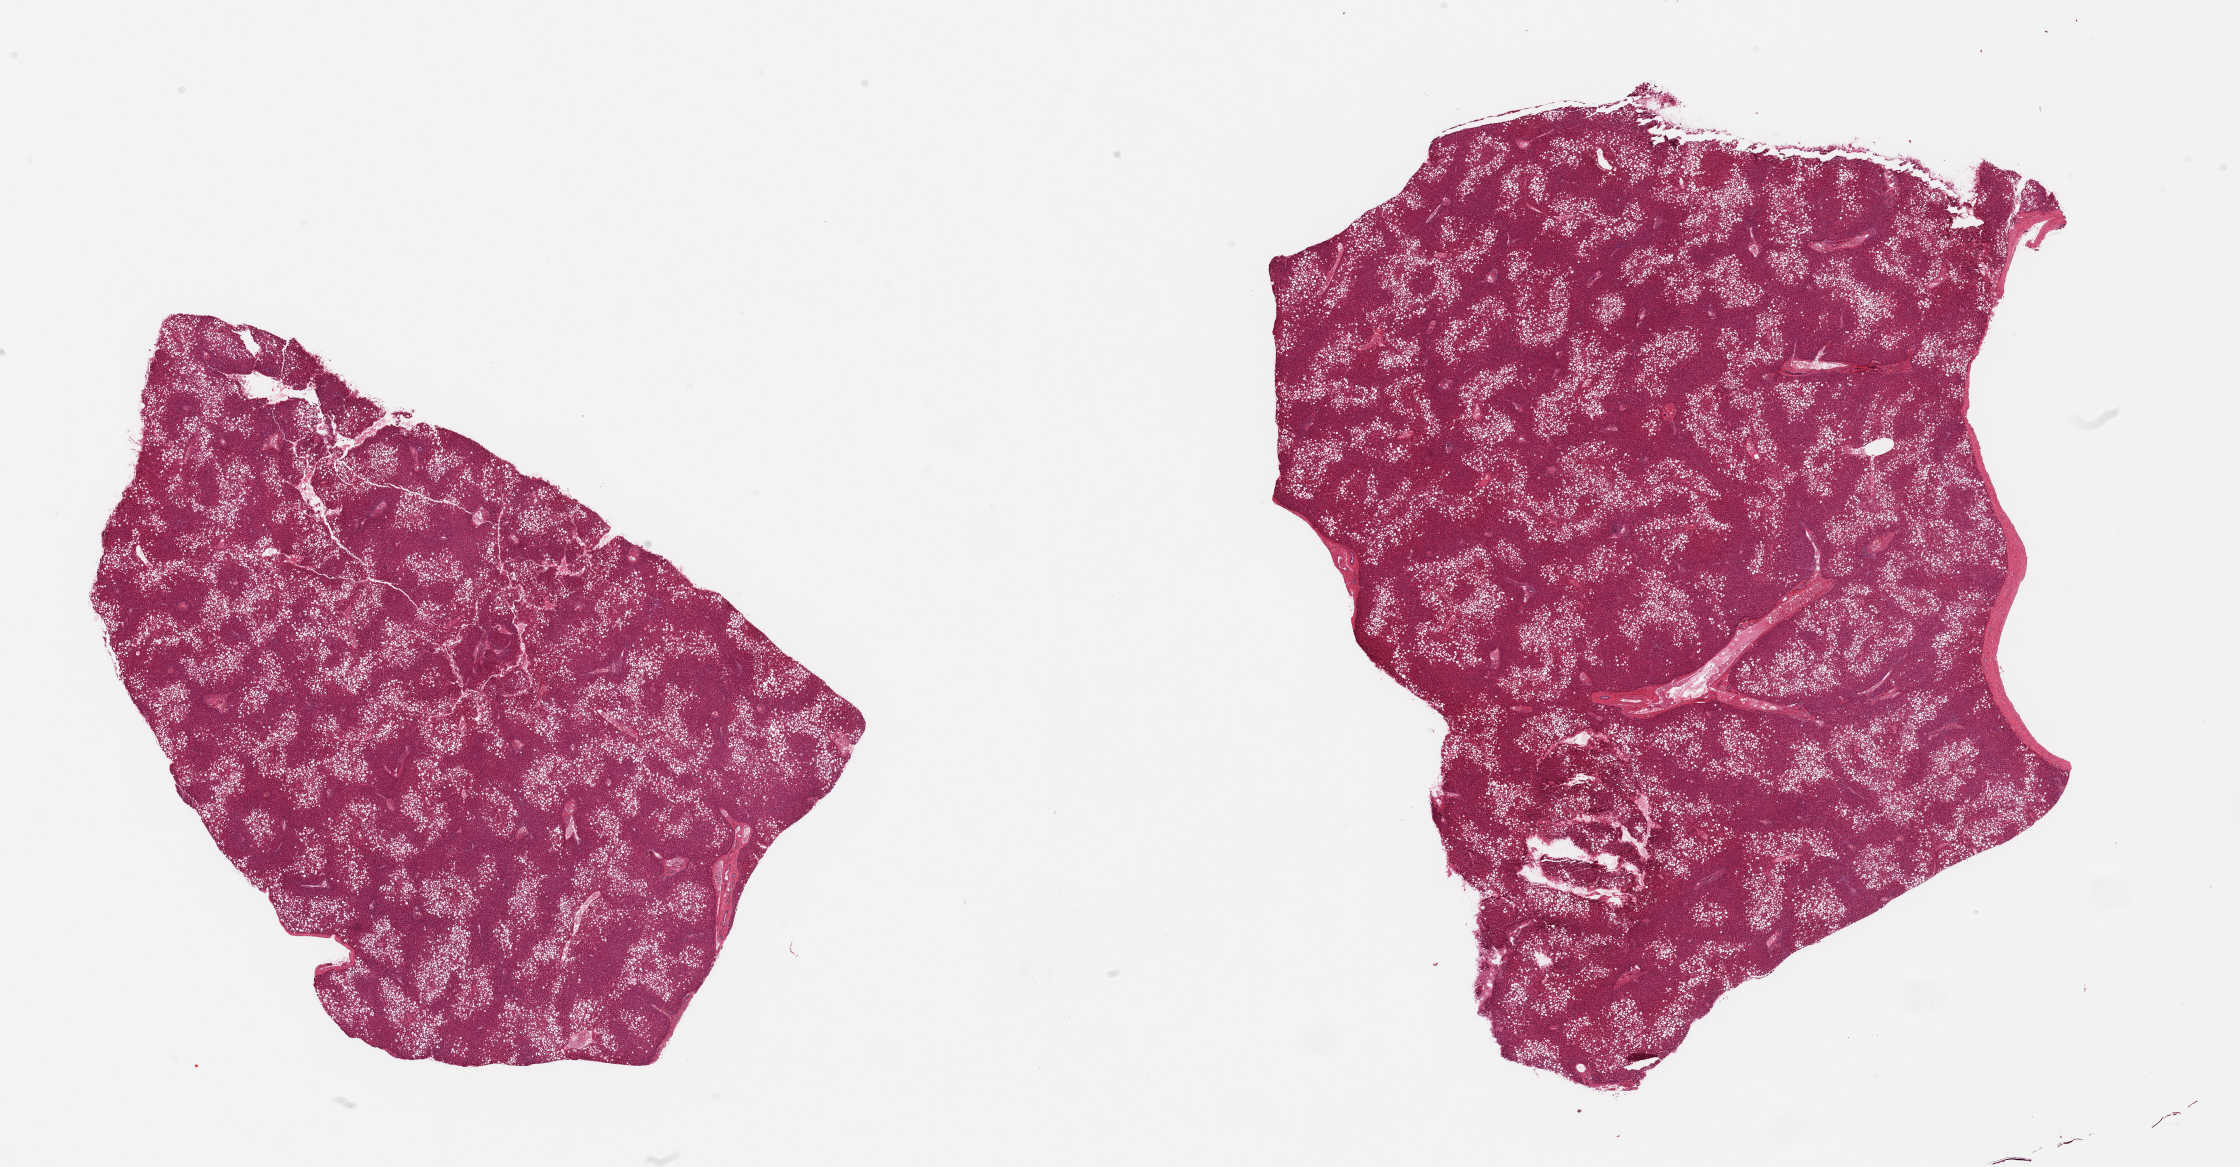
H&E whole-slide image, low-resolution overview of the scanned area, about 35.4 x 18.5 mm, PAXgene-fixed paraffin-embedded (PFPE) section, sampled site (target tissue): liver, donor tissue sample.
Pathologist's review note for this sample: 2 pieces; 50% macrosteatosis.